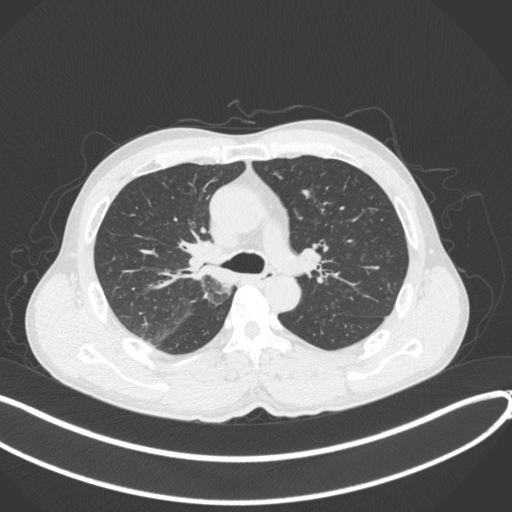
Chest CT, one axial slice. Position 254 of 409 along the scan axis. 120 kVp. Lung window (W 1500 / L -600 HU). 1 mm slice thickness. 512 × 512 image matrix, field of view 400 × 400 mm. Patient: male, 53 years. From the clinical record (not read from this slice): clinical TNM (as recorded): T1b N0 M0.
Structures marked on this image (rectangle marked by the reading radiologist):
- lung tumour (recorded histology: squamous cell carcinoma): bounding box [x1, y1, x2, y2] px = [180, 238, 222, 290]